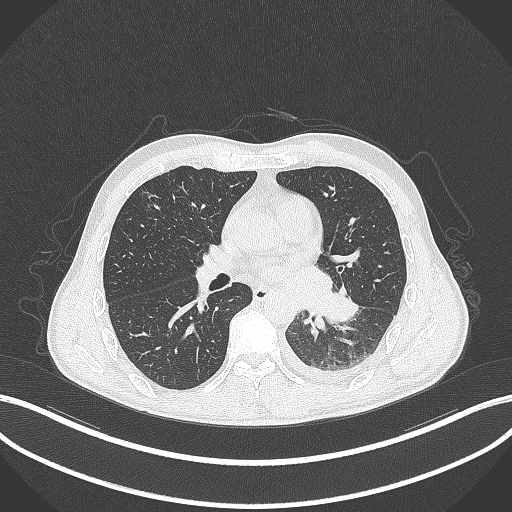
Chest CT, one axial slice. Position 162 of 295 along the scan axis. Reconstruction kernel B70f. Lung window (W 1500 / L -600 HU). 1 mm slice thickness. 512 × 512 image matrix, field of view 400 × 400 mm. Patient: male, 47 years. From the clinical record (not read from this slice): clinical TNM (as recorded): T3 N1 M1c.
Annotated regions visible in this slice (bounding box drawn by a radiologist):
- lung tumour (recorded histology: small cell carcinoma): bounding box (x1, y1, x2, y2) in pixels: (314, 287, 362, 325)